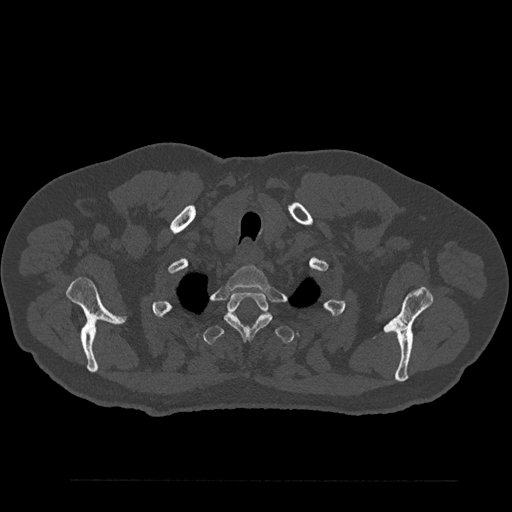
CT including the spine, one axial slice. Reconstruction kernel Br40s/3. Bone window (W 1800 / L 400 HU). 0.5 mm slice thickness. 512 × 512 image matrix. Patient: male, 61 years. Case-level facts recorded for this patient, not image findings: primary cancer: prostate.
Annotated regions visible in this slice (semi-automatic segmentation, software-assisted and operator-edited):
- T1 vertebra: bounding box [x1, y1, x2, y2] px = [227, 266, 270, 290]
- T2 vertebra: [224, 292, 272, 340]
- T3 vertebra: [204, 325, 295, 345]